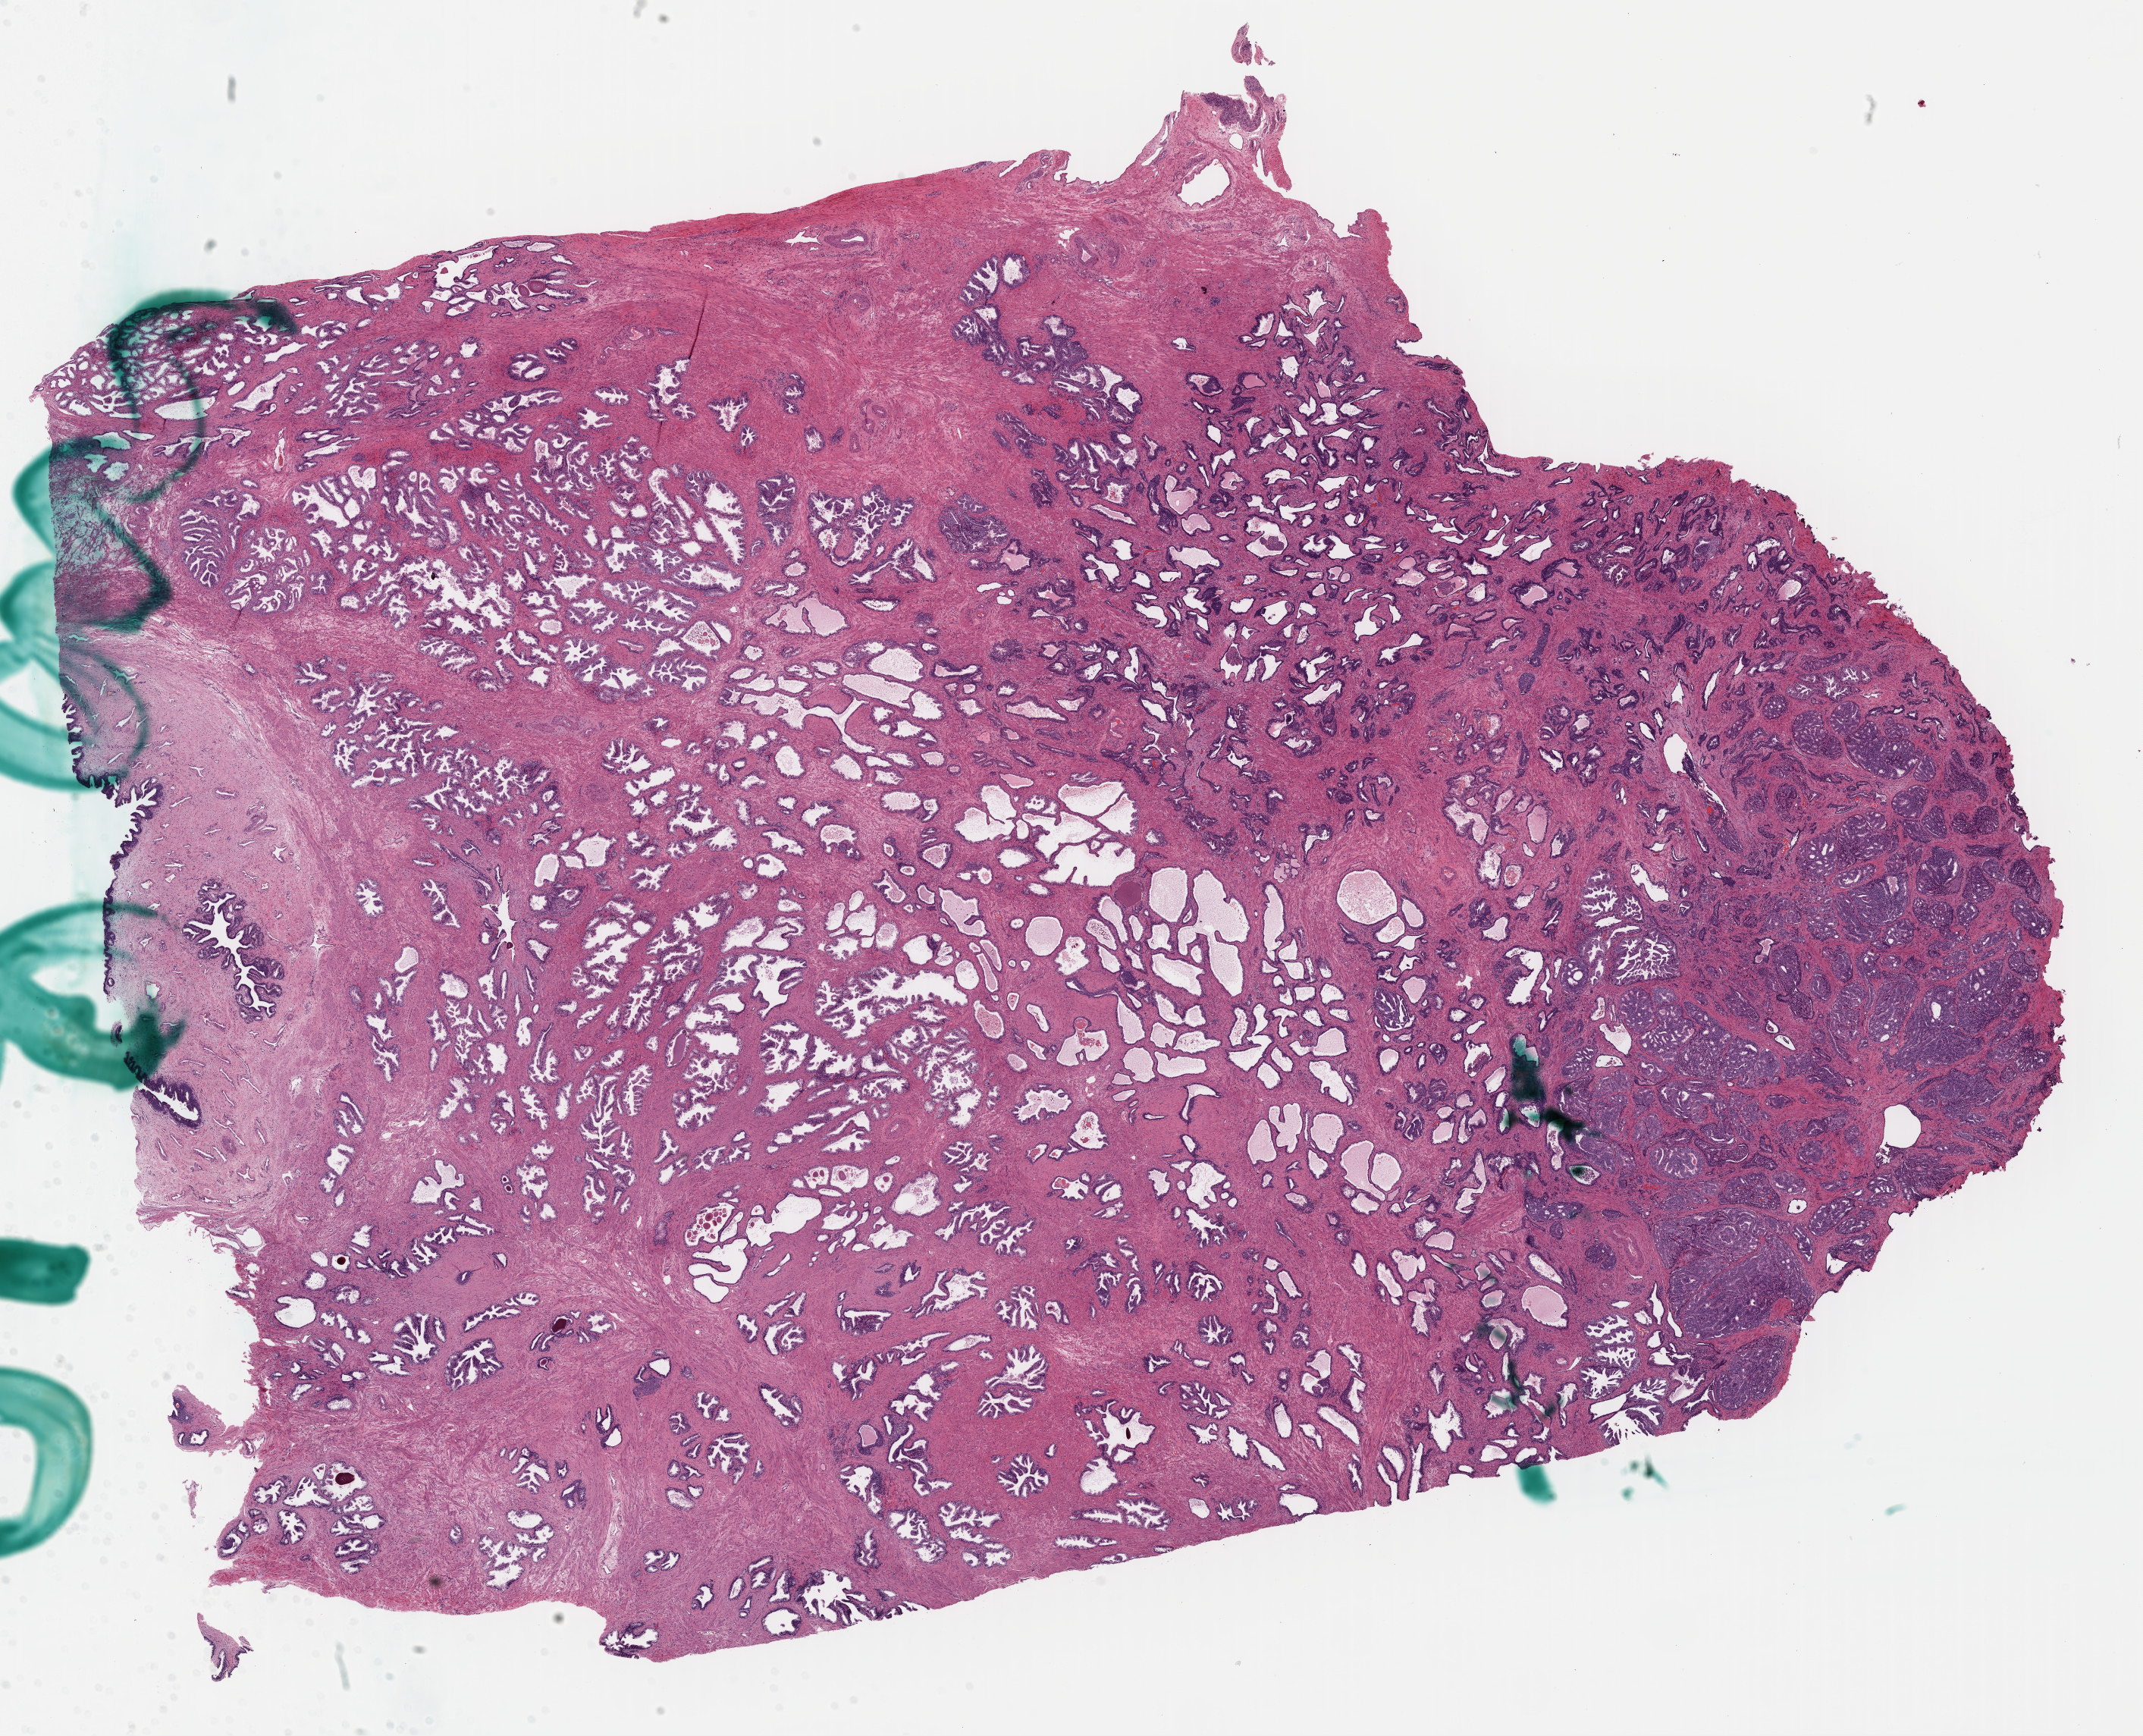
Digitized H&E-stained tissue section (whole slide) — low-resolution overview of the scanned area, about 22.2 x 18.0 mm; formalin-fixed paraffin-embedded (FFPE) diagnostic section; prostate, primary tumour sample. Male patient; age at initial diagnosis 57 years. Gleason score: 8 (4+4).
• diagnosis: Adenocarcinoma, NOS (prostate gland)
• laterality: bilateral